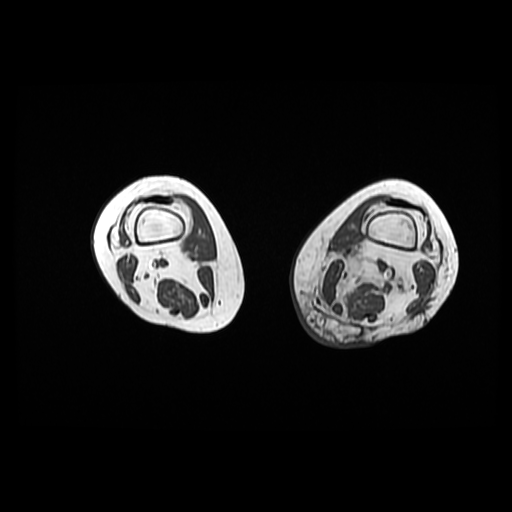
MRI of an extremity soft-tissue mass, one axial slice; slice 16 of 42 in the series (ordered by position); 6 mm slice thickness; 512 × 512 image matrix. Female patient. Case-level facts recorded for this patient, not image findings: histological type: pleomorphic leiomyosarcoma; grade: high; site of the primary tumour: left thigh.
Annotated regions visible in this slice (outlined manually by an expert reader):
- gross tumour volume including surrounding oedema: box from (x=311, y=251) to (x=411, y=312) px